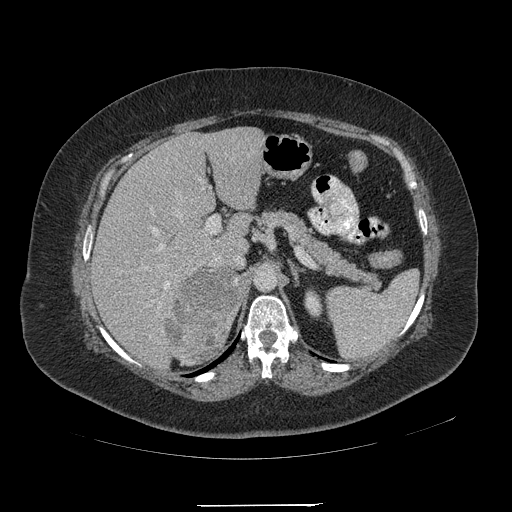
Contrast-enhanced abdominal CT, one axial slice; slice 139 of 217 in the series (ordered by position); 120 kVp; intravenous contrast given; soft-tissue window (W 400 / L 40 HU); 512 × 512 image matrix, field of view 453 × 453 mm. Female patient, age 55 years. Case-level facts recorded for this patient, not image findings: diagnosis: adrenocortical carcinoma; tumour side: right adrenal; tumour size at pathology: 11 cm; Ki-67 index: 20 %; stage (as recorded): 2.
Structures marked on this image (semi-automatic segmentation, software-assisted and operator-edited):
- mass: box from (x=164, y=268) to (x=242, y=359) px